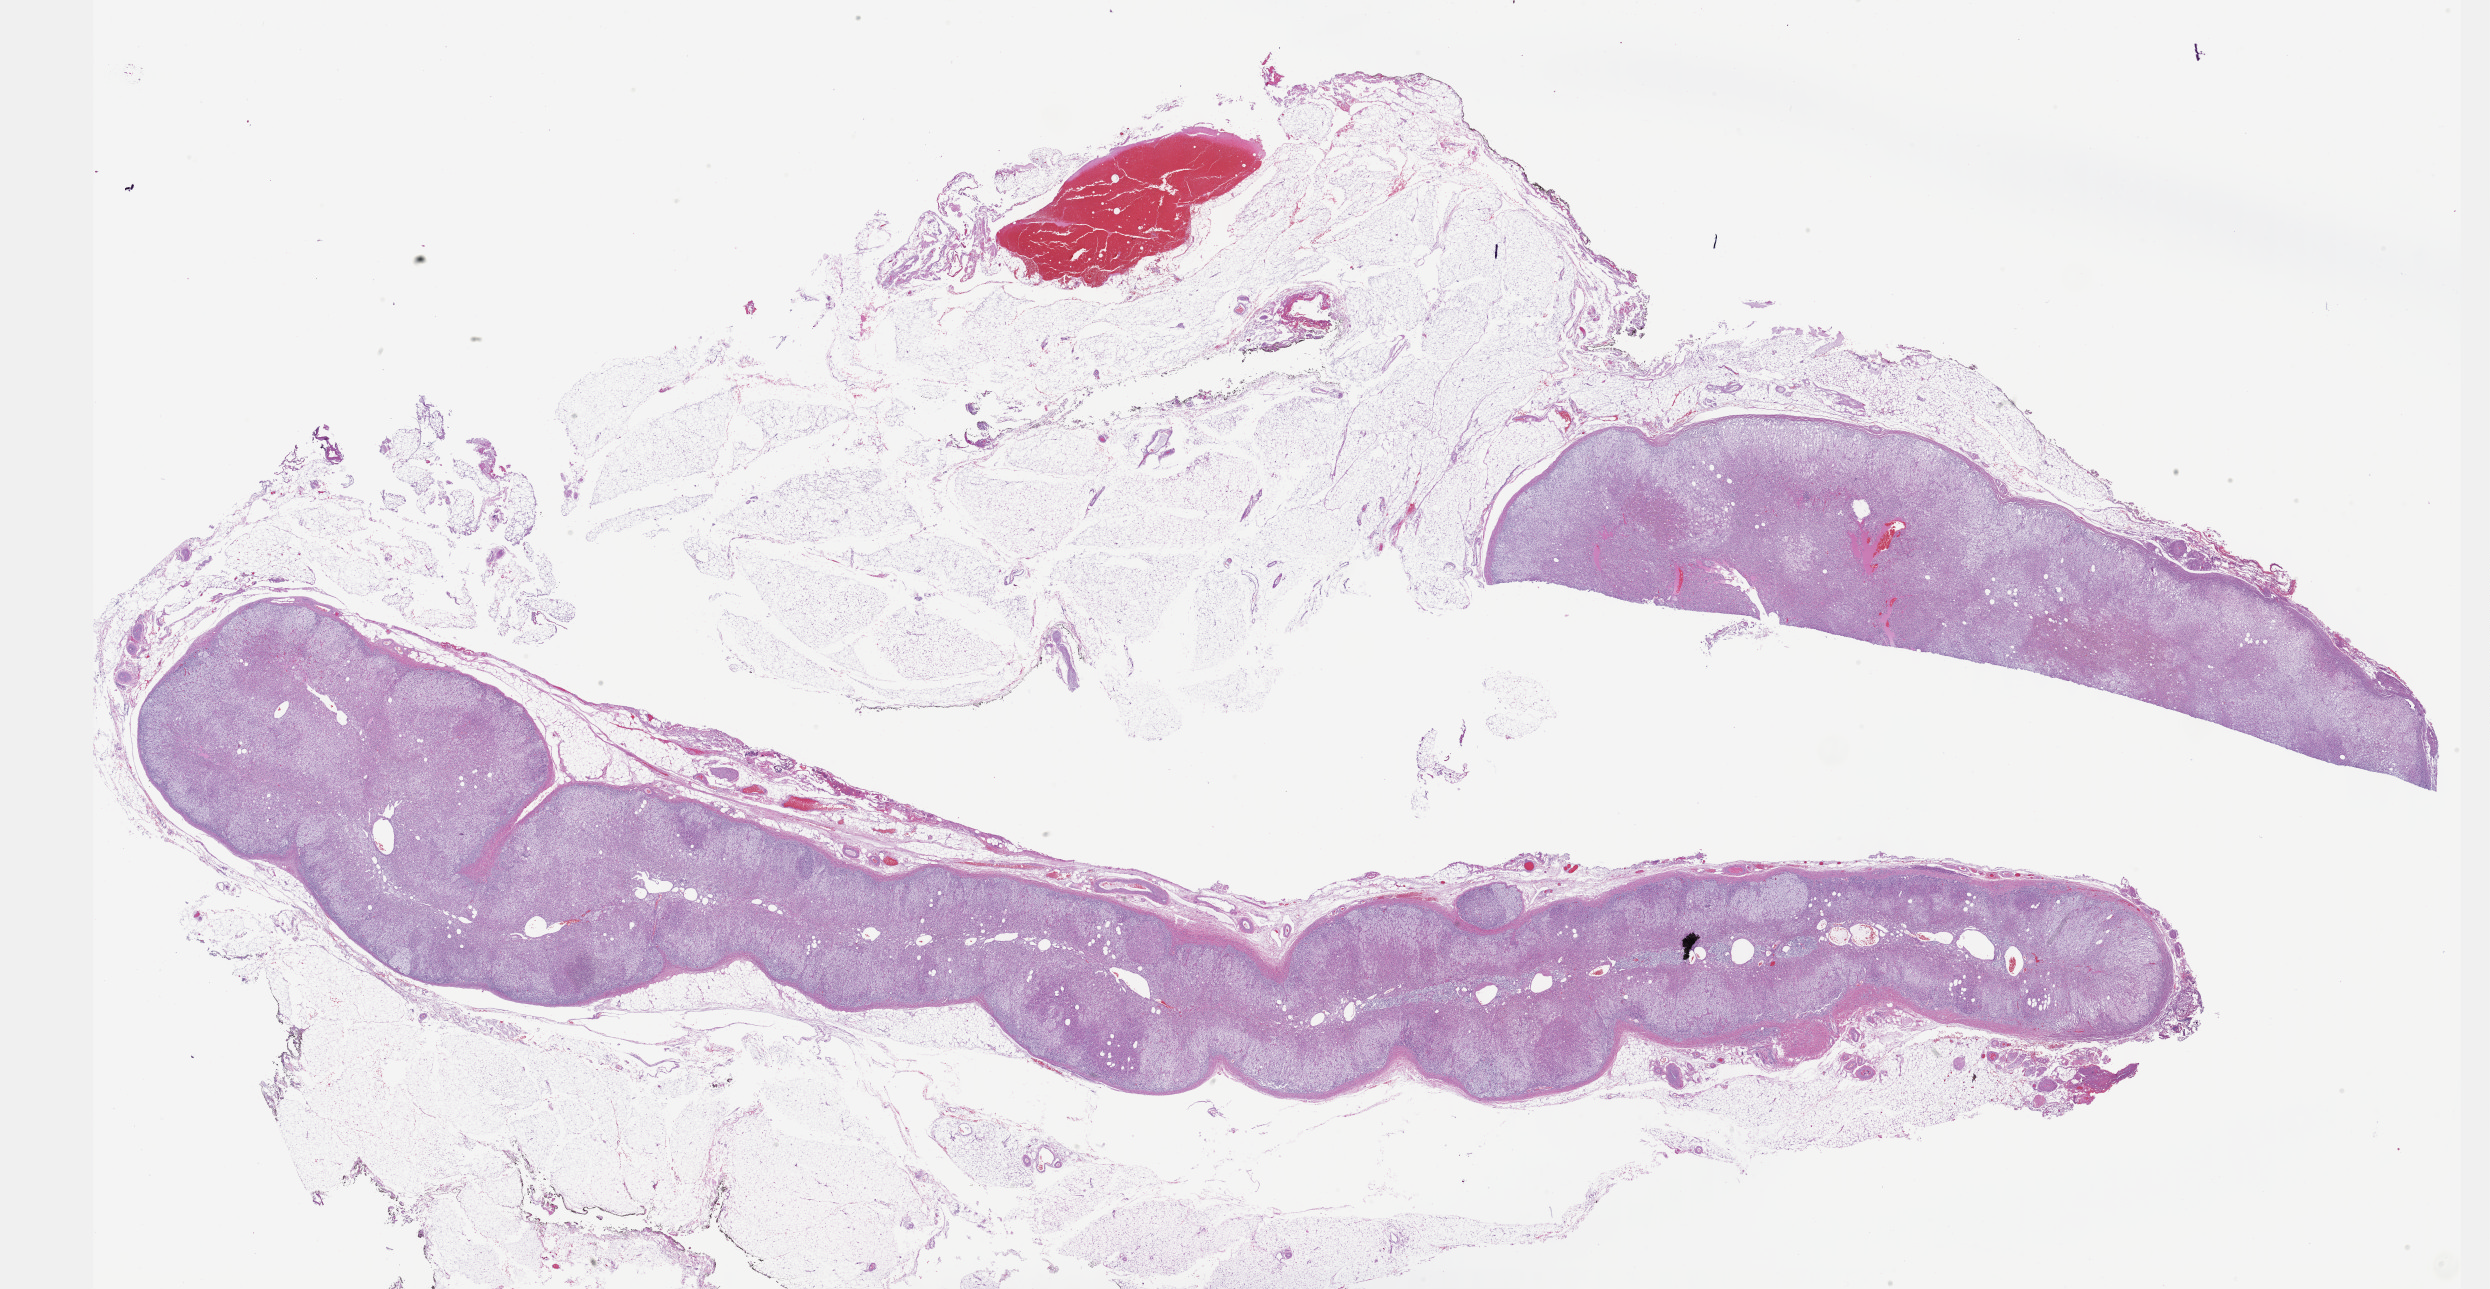
Digitized Hematoxylin and eosin (H&E) stained tissue section (whole slide), shown as a low-resolution overview of the whole scanned area (about 40.2 x 20.8 mm, from a 40x scan). Formalin-fixed paraffin-embedded (FFPE) diagnostic section. Primary tumour sample from the adrenal gland. Patient: female, age at initial diagnosis 52 years.
Pathologic diagnosis: Pheochromocytoma, NOS. Laterality: right.